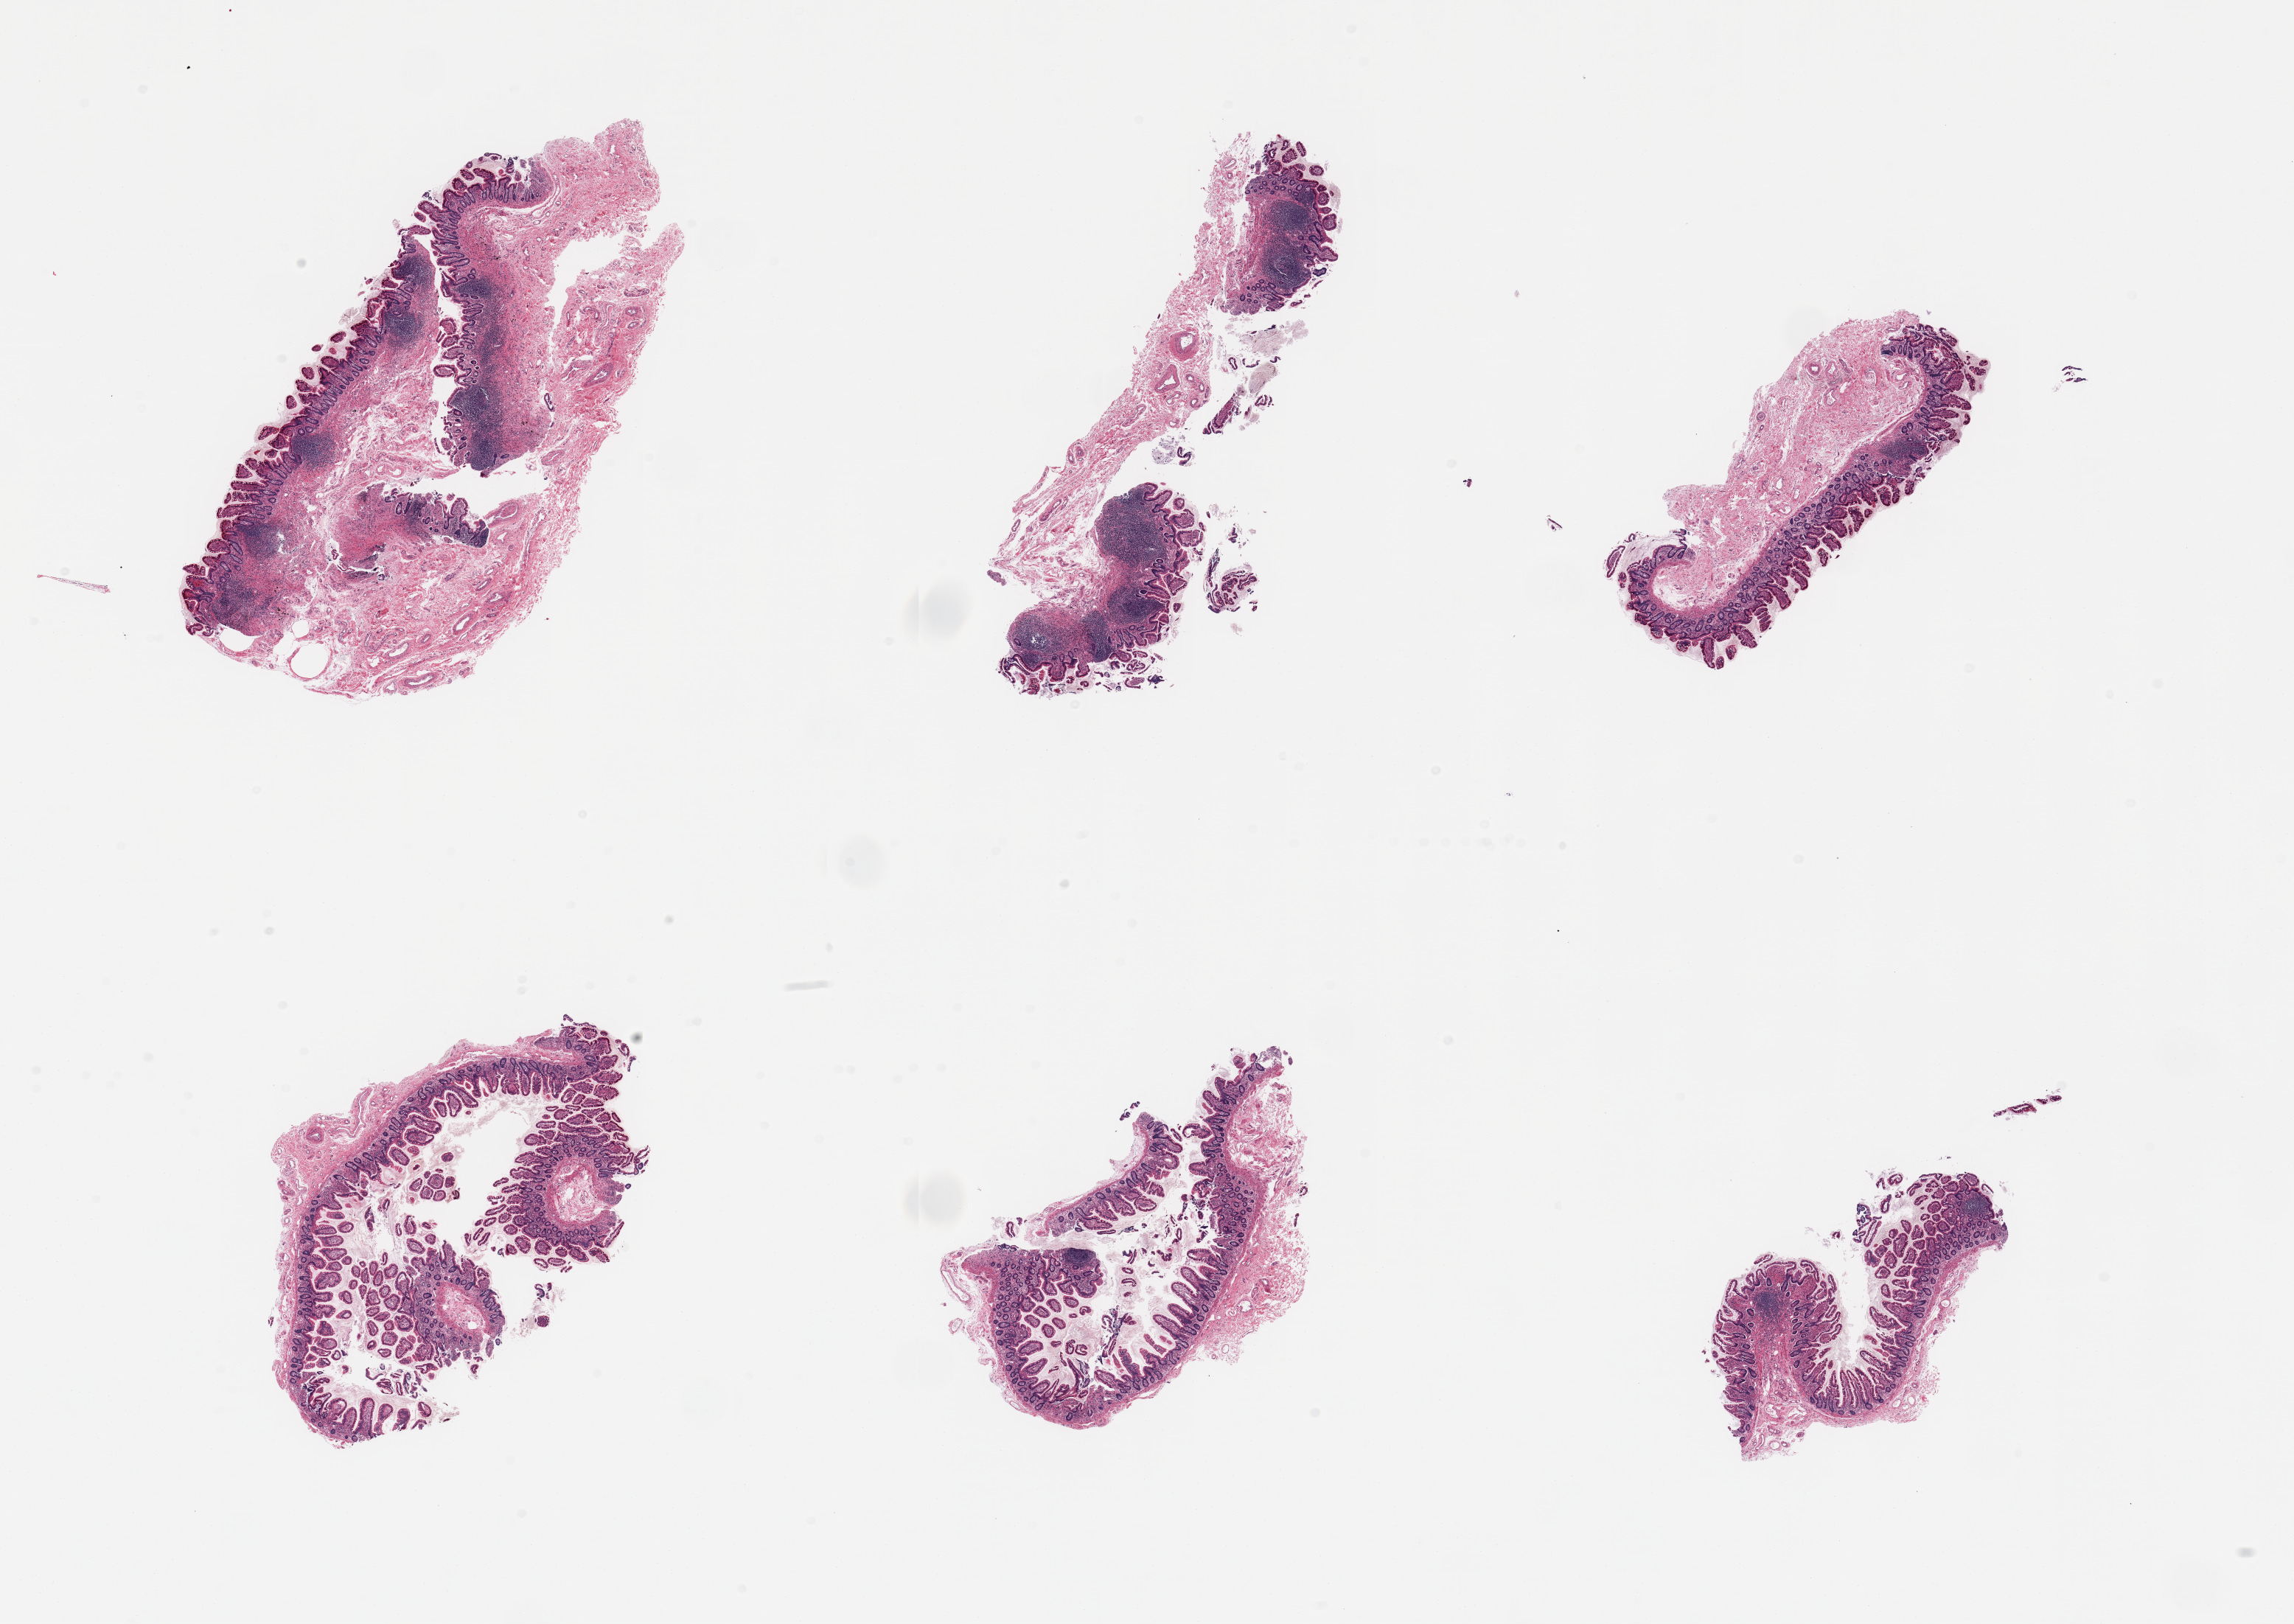
Digitized H&E-stained section — low-resolution overview of the scanned area, about 24.6 x 17.4 mm (slide scanned at 20x). PAXgene-fixed paraffin-embedded (PFPE) section. Sampled site (target tissue): ileum. Donor tissue sample. Donor sex: male.
Pathologist's review note for this sample: 6 pieces; several lymphoid nodules in well preserved mucosa.